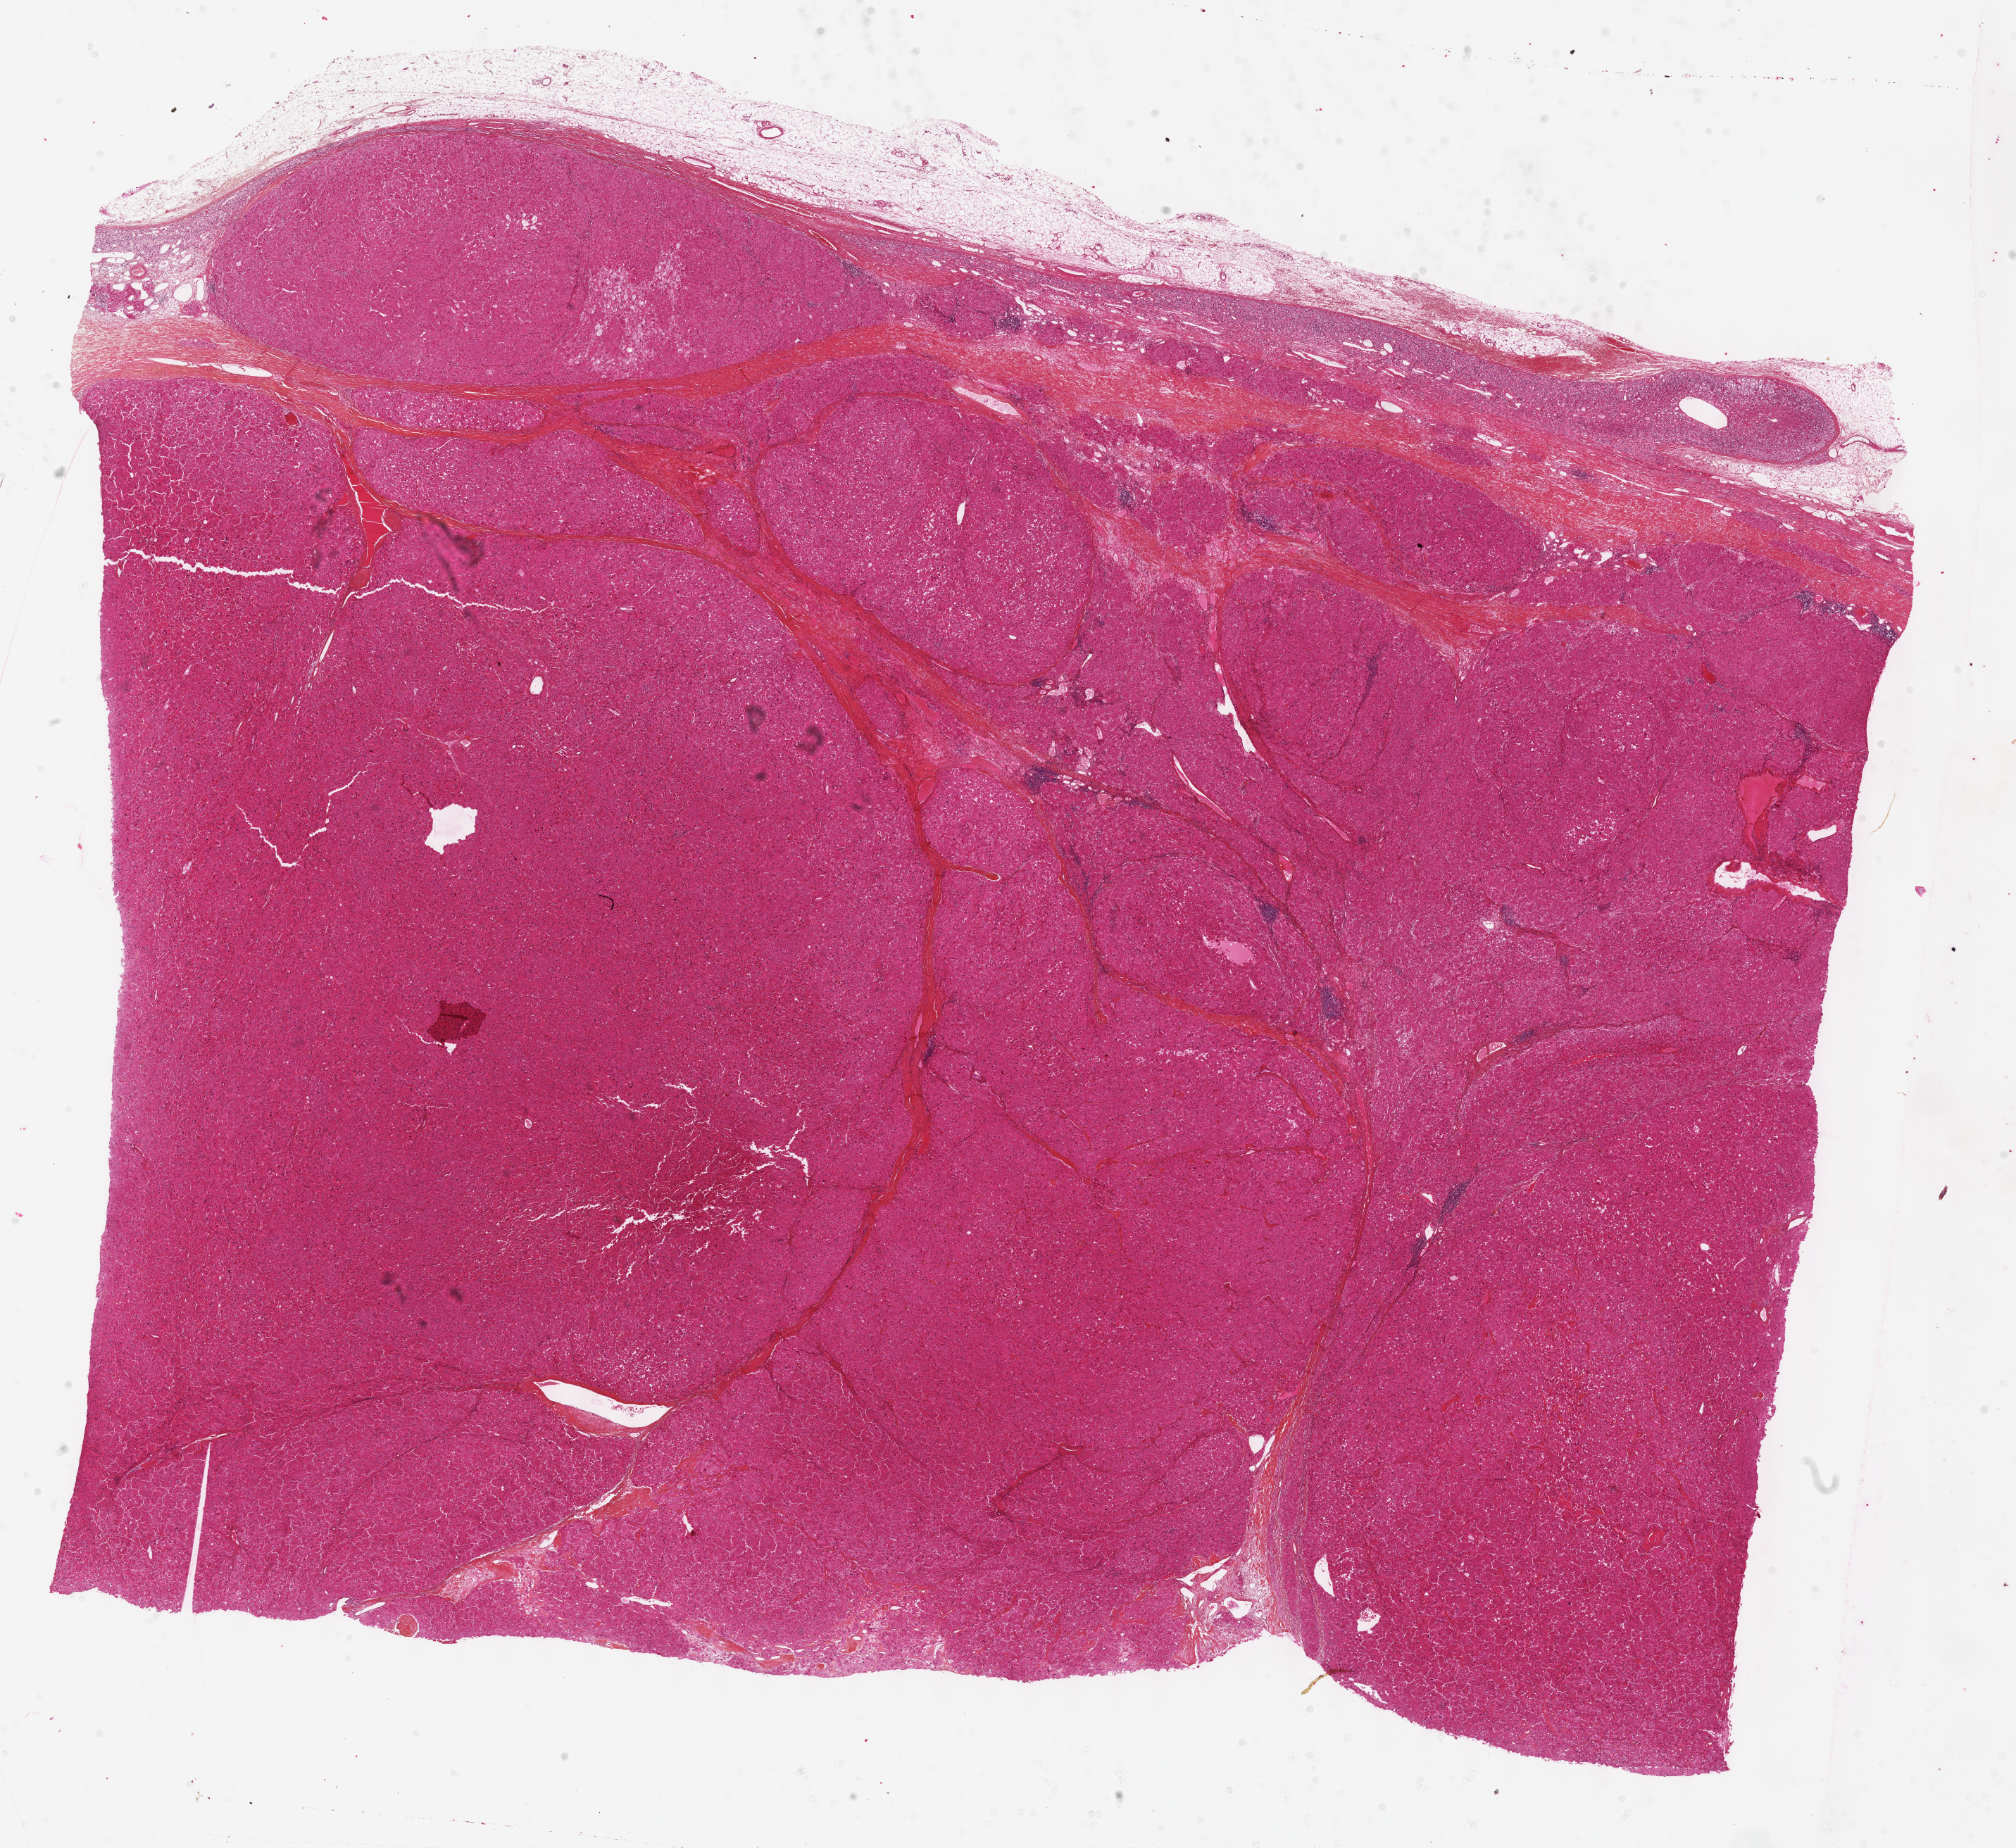
Hematoxylin and eosin (H&E) stained whole-slide image, low-resolution overview of the scanned area, about 23.1 x 21.2 mm, formalin-fixed paraffin-embedded (FFPE) diagnostic section, primary tumour sample from the adrenal cortex. Female, age 37 years at initial diagnosis.
• lymph nodes positive (case pathology): 0 of 21 examined
• histologic diagnosis: Adrenal cortical carcinoma (cortex of adrenal gland)